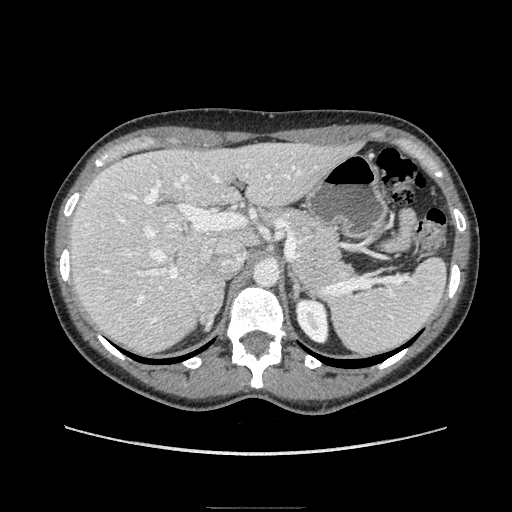
Contrast-enhanced abdominal CT, one axial slice. Slice 120 of 193 in the series (ordered by position). Soft-tissue window (W 400 / L 40 HU). 1.25 mm slice thickness. 512 × 512 image matrix, field of view 380 × 380 mm. Female patient. From the clinical record (not read from this slice): diagnosis: adrenocortical carcinoma; tumour side: right adrenal; tumour size at pathology: 3 cm; Ki-67 index: 4 %; stage (as recorded): 1.
Annotated regions visible in this slice (semi-automatic segmentation, software-assisted and operator-edited):
- mass: bounding box (x1, y1, x2, y2) in pixels: (194, 280, 223, 328)